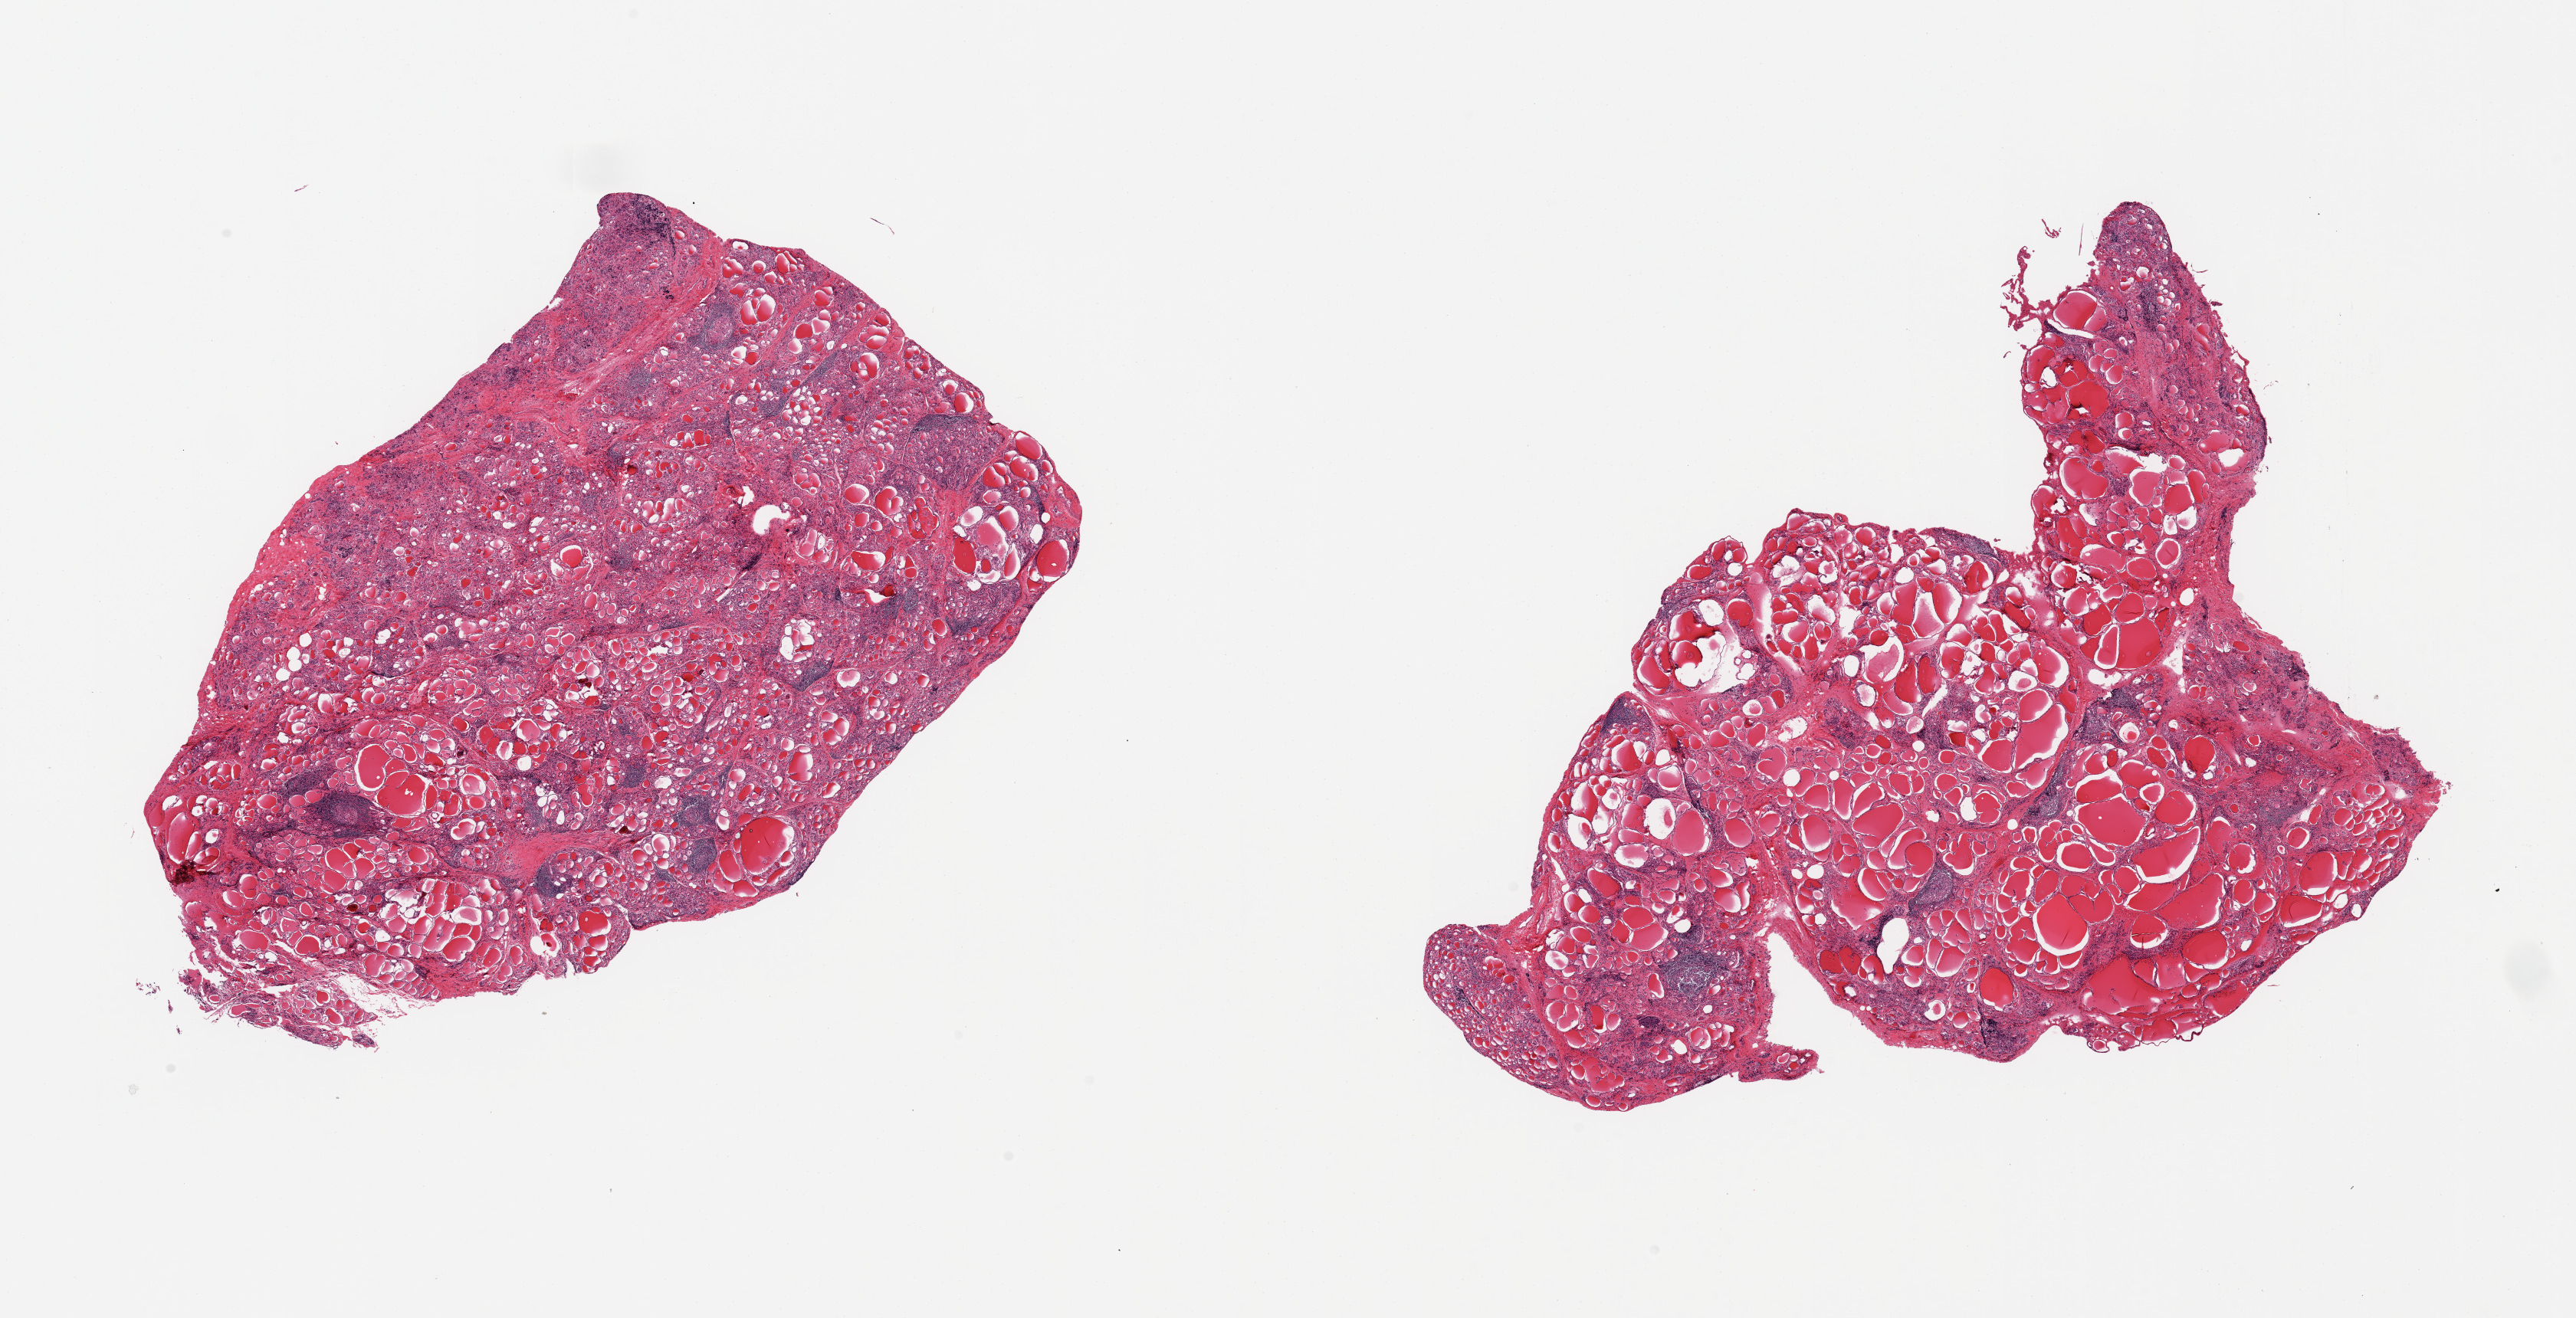
H&E whole-slide image — whole scanned area (about 26.6 x 13.6 mm) shown as a low-resolution overview. PAXgene-fixed paraffin-embedded (PFPE) section. Sampled site (target tissue): thyroid. Donor tissue sample. Donor: male.
Reviewer comment on this tissue sample: 2 pieces; moderate lymphoid content consistent with lymphocytic (Hashimoto) thyroiditis.